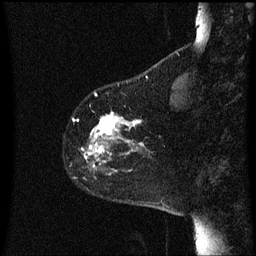
Breast MRI (dynamic contrast-enhanced), one sagittal slice; position 12 of 60 along the scan axis; dynamic contrast-enhanced series, image 2 of 3 at this slice position (ordered by acquisition); 1.5 T; TE 4.2 ms, TR 8 ms; 256 × 256 image matrix. Patient: female, 60 years.
Outlined on this slice (semi-automatically segmented with operator editing):
- analysis volume of interest (the breast-tissue region the enhancement analysis was run in; not a lesion): bounding box <82,112,145,179> (left, top, right, bottom; pixels)
- tumour enhancement mask (voxels above the 70 % enhancement threshold inside the analysis volume of interest): <82,112,140,167>